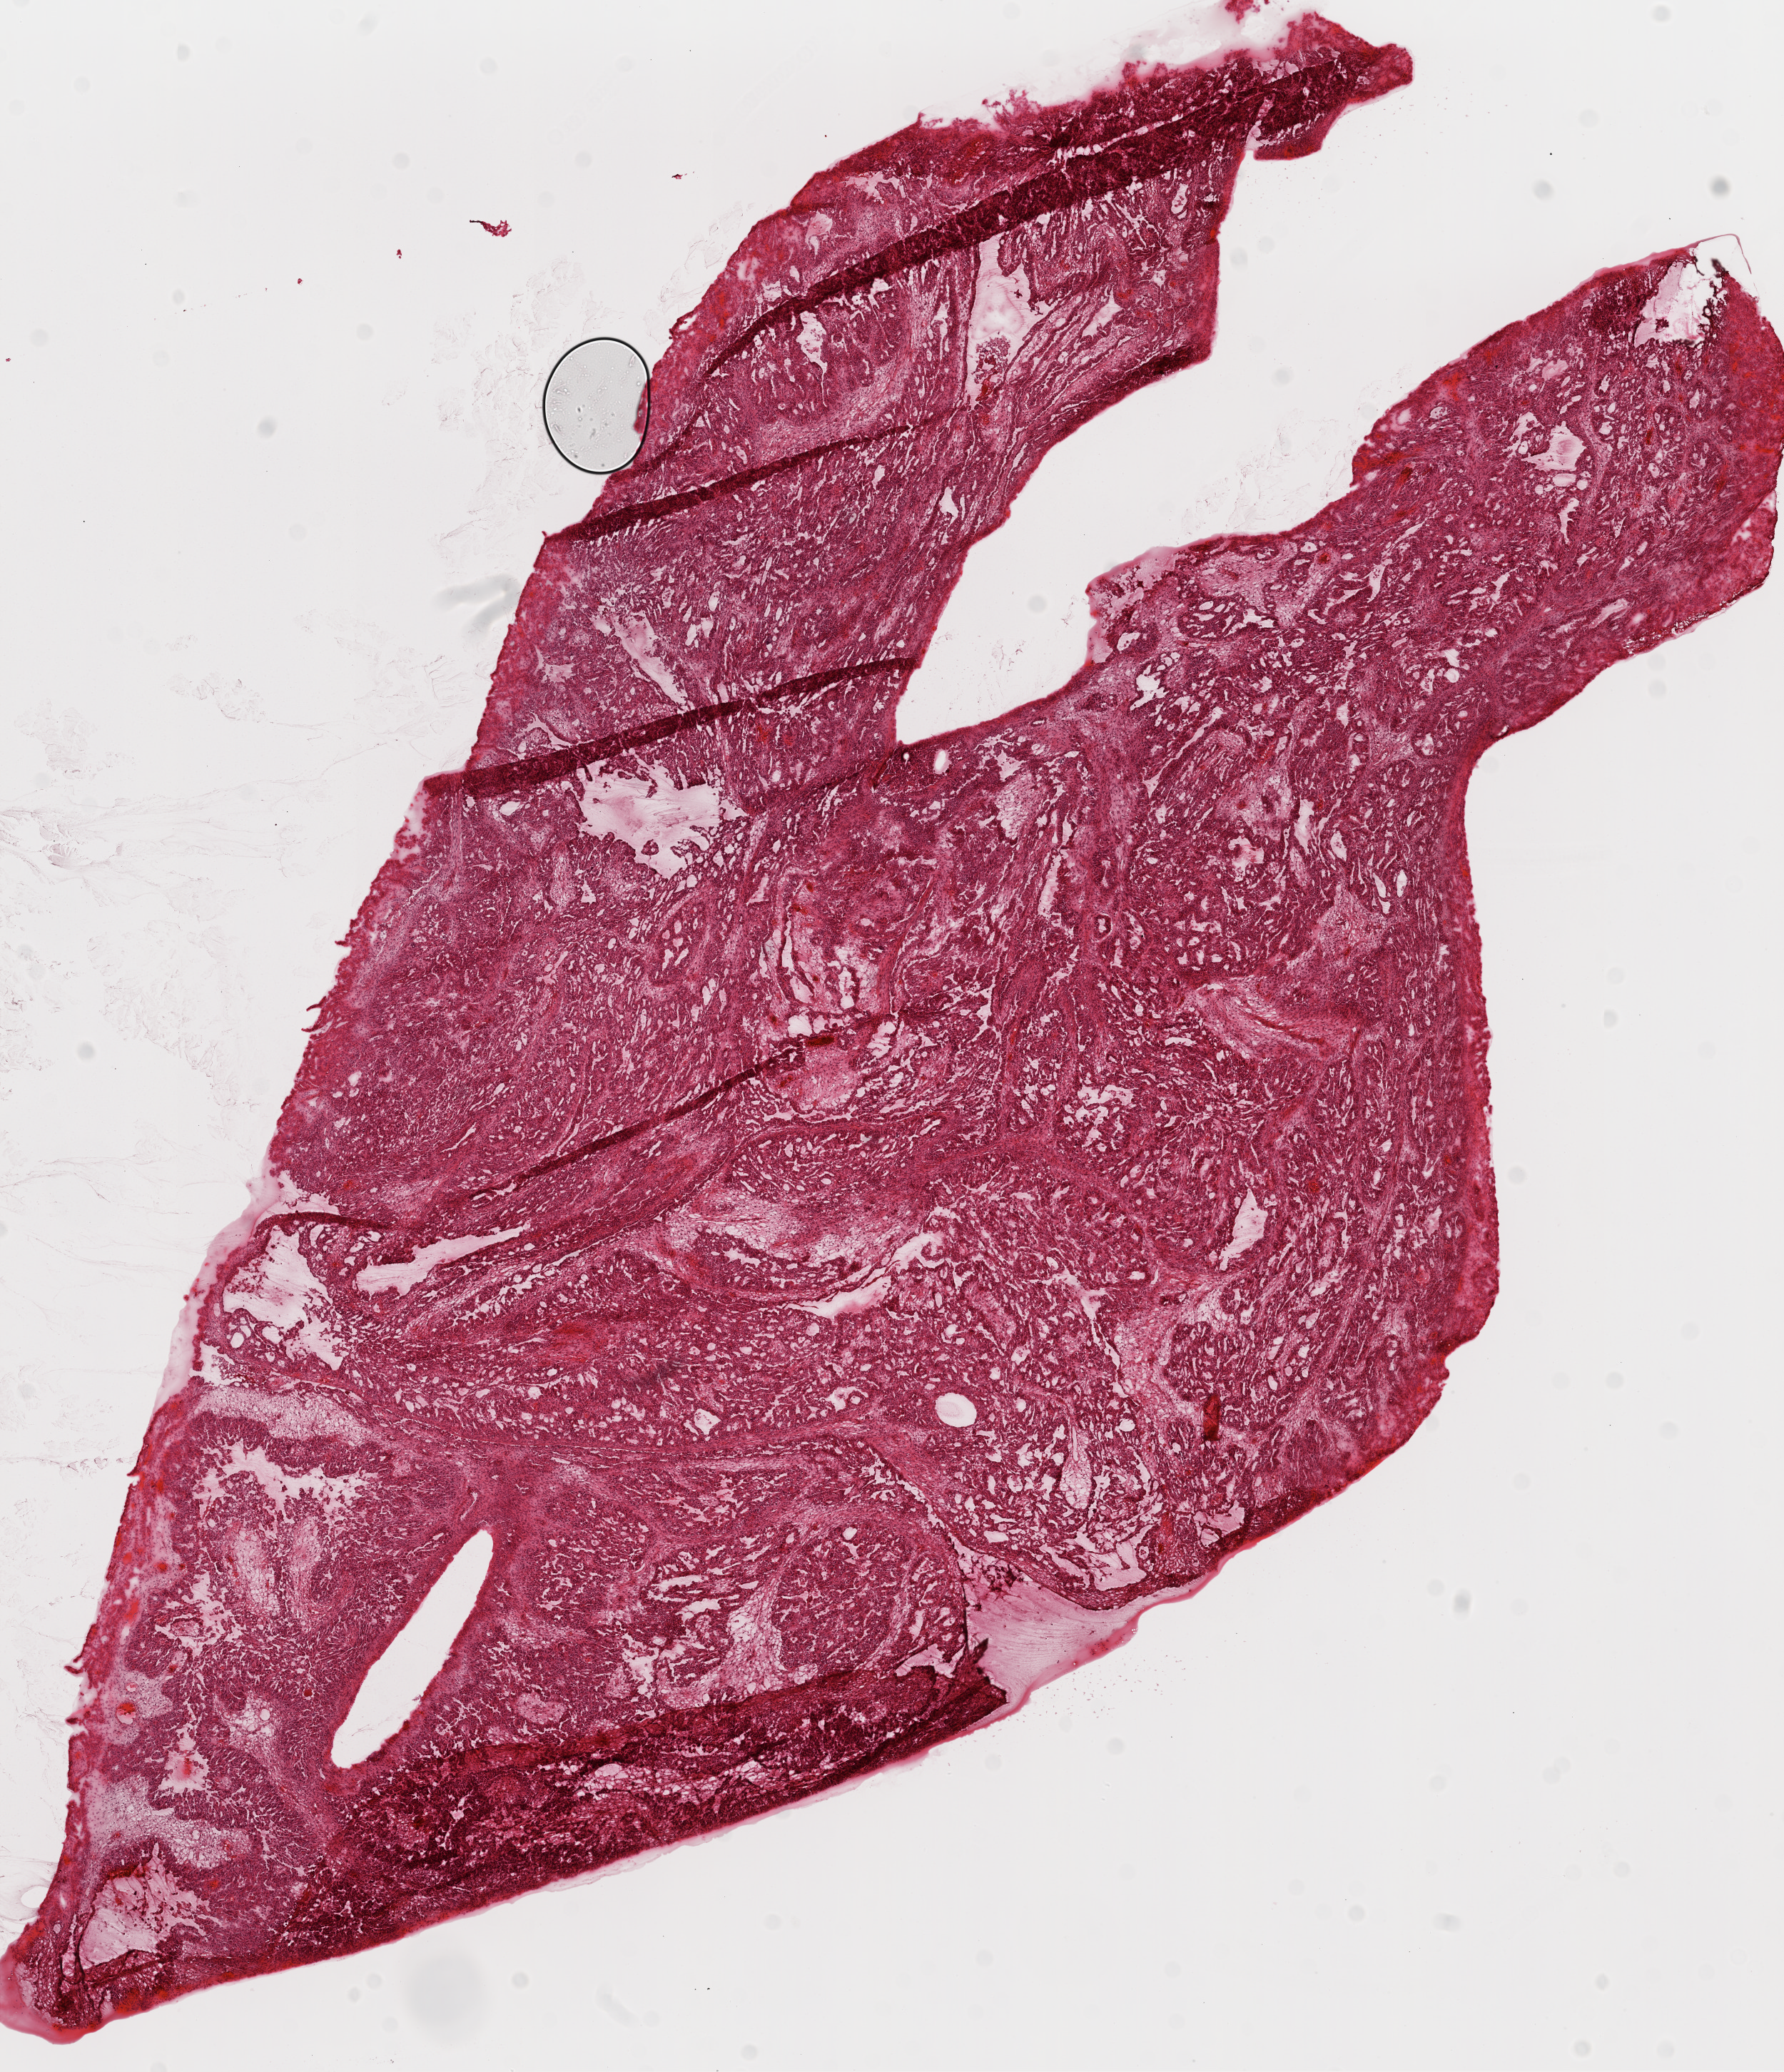
Whole-slide histology image, Hematoxylin and eosin (H&E) stained, whole scanned area (about 10.0 x 11.7 mm, slide scanned at 20x) shown as a low-resolution overview; frozen section from the top of the tissue portion; sample: primary tumour, ovary. Female, age 34 years at initial diagnosis. Histologic grade: G3 (poorly differentiated). Pathologist review of this section (percent, as recorded): tumour cells 55%, tumour nuclei 80%, normal cells 40%, stromal cells 0%, necrosis 5%.
- FIGO stage: IV
- pathologic diagnosis: Serous cystadenocarcinoma, NOS